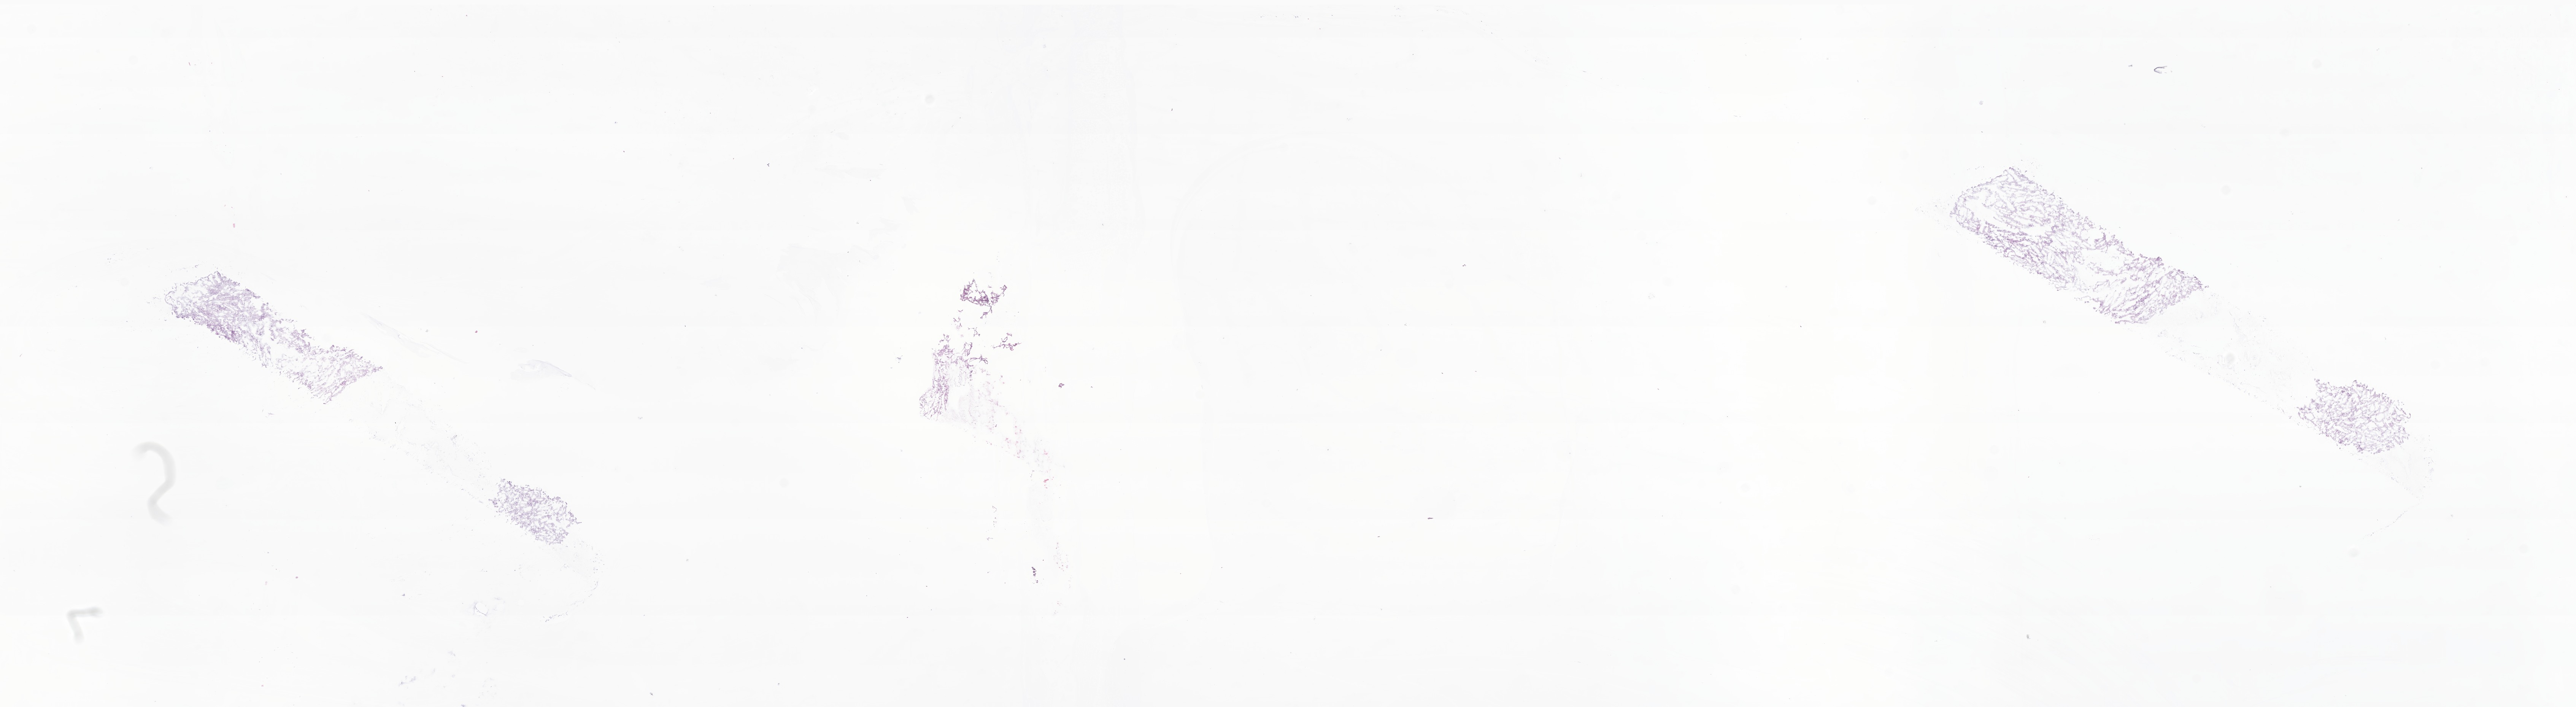
Whole-slide image, hematoxylin and eosin (H&E) stain of tumor tissue from the cerebellum — a low-resolution overview of the entire scanned area, about 28.6 x 7.8 mm; cryosection (OCT / tissue freezing medium). Patient: female, age 61 months (5 years 1 month).
• diagnosis: Astrocytoma, NOS